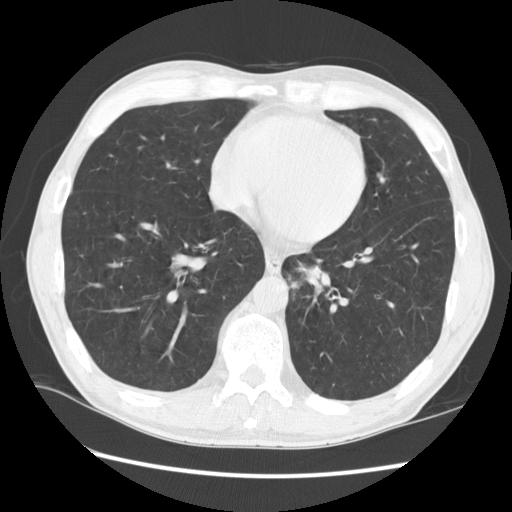
Chest CT (low-dose screening protocol), one axial image; baseline annual screen; lung window (W 1500 / L -600 HU); standard (soft-tissue) reconstruction kernel (STANDARD); slice 95 of 141 in the series. Male participant, aged 57 years at enrolment. Current smoker at enrolment.
• Lesion marked by an expert reader, bounding box <268,247,343,312> (left, top, right, bottom; pixels).
• The screening reader recorded 2 non-calcified nodules or masses ≥4 mm on this exam (left lower lobe, lingula); which of them this box marks is not recorded.
• Official screen result: positive, change unspecified: nodule(s) >= 4 mm or enlarging nodule(s), mass(es), or other non-specific abnormalities suspicious for lung cancer.
• Lung cancer was diagnosed 95 days after this screen: squamous cell carcinoma, NOS, left lower lobe, moderately differentiated (G2), stage IB (AJCC 6th edition), 35 mm at pathology.